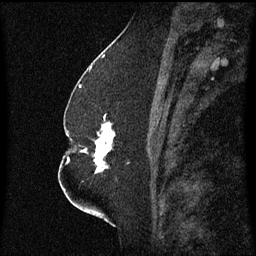
Breast MRI (dynamic contrast-enhanced), one sagittal slice; slice 29 of 60 in the series (ordered by position); dynamic contrast-enhanced series, image 2 of 3 at this slice position (ordered by acquisition); 1.5 T; TE 4.2 ms, TR 8.4 ms; 2.3 mm slice thickness; 256 × 256 image matrix, field of view 200 × 200 mm. Patient: female, 52 years. Case-level facts recorded for this patient, not image findings: setting: breast cancer imaged before/during neoadjuvant chemotherapy; receptor status: HR-positive, HER2-negative.
Annotated regions visible in this slice (semi-automatically segmented with operator editing):
- analysis volume of interest (the breast-tissue region the enhancement analysis was run in; not a lesion): bounding box <82,122,129,175> (left, top, right, bottom; pixels)
- tumour enhancement mask (voxels above the 70 % enhancement threshold inside the analysis volume of interest): <85,122,115,175>